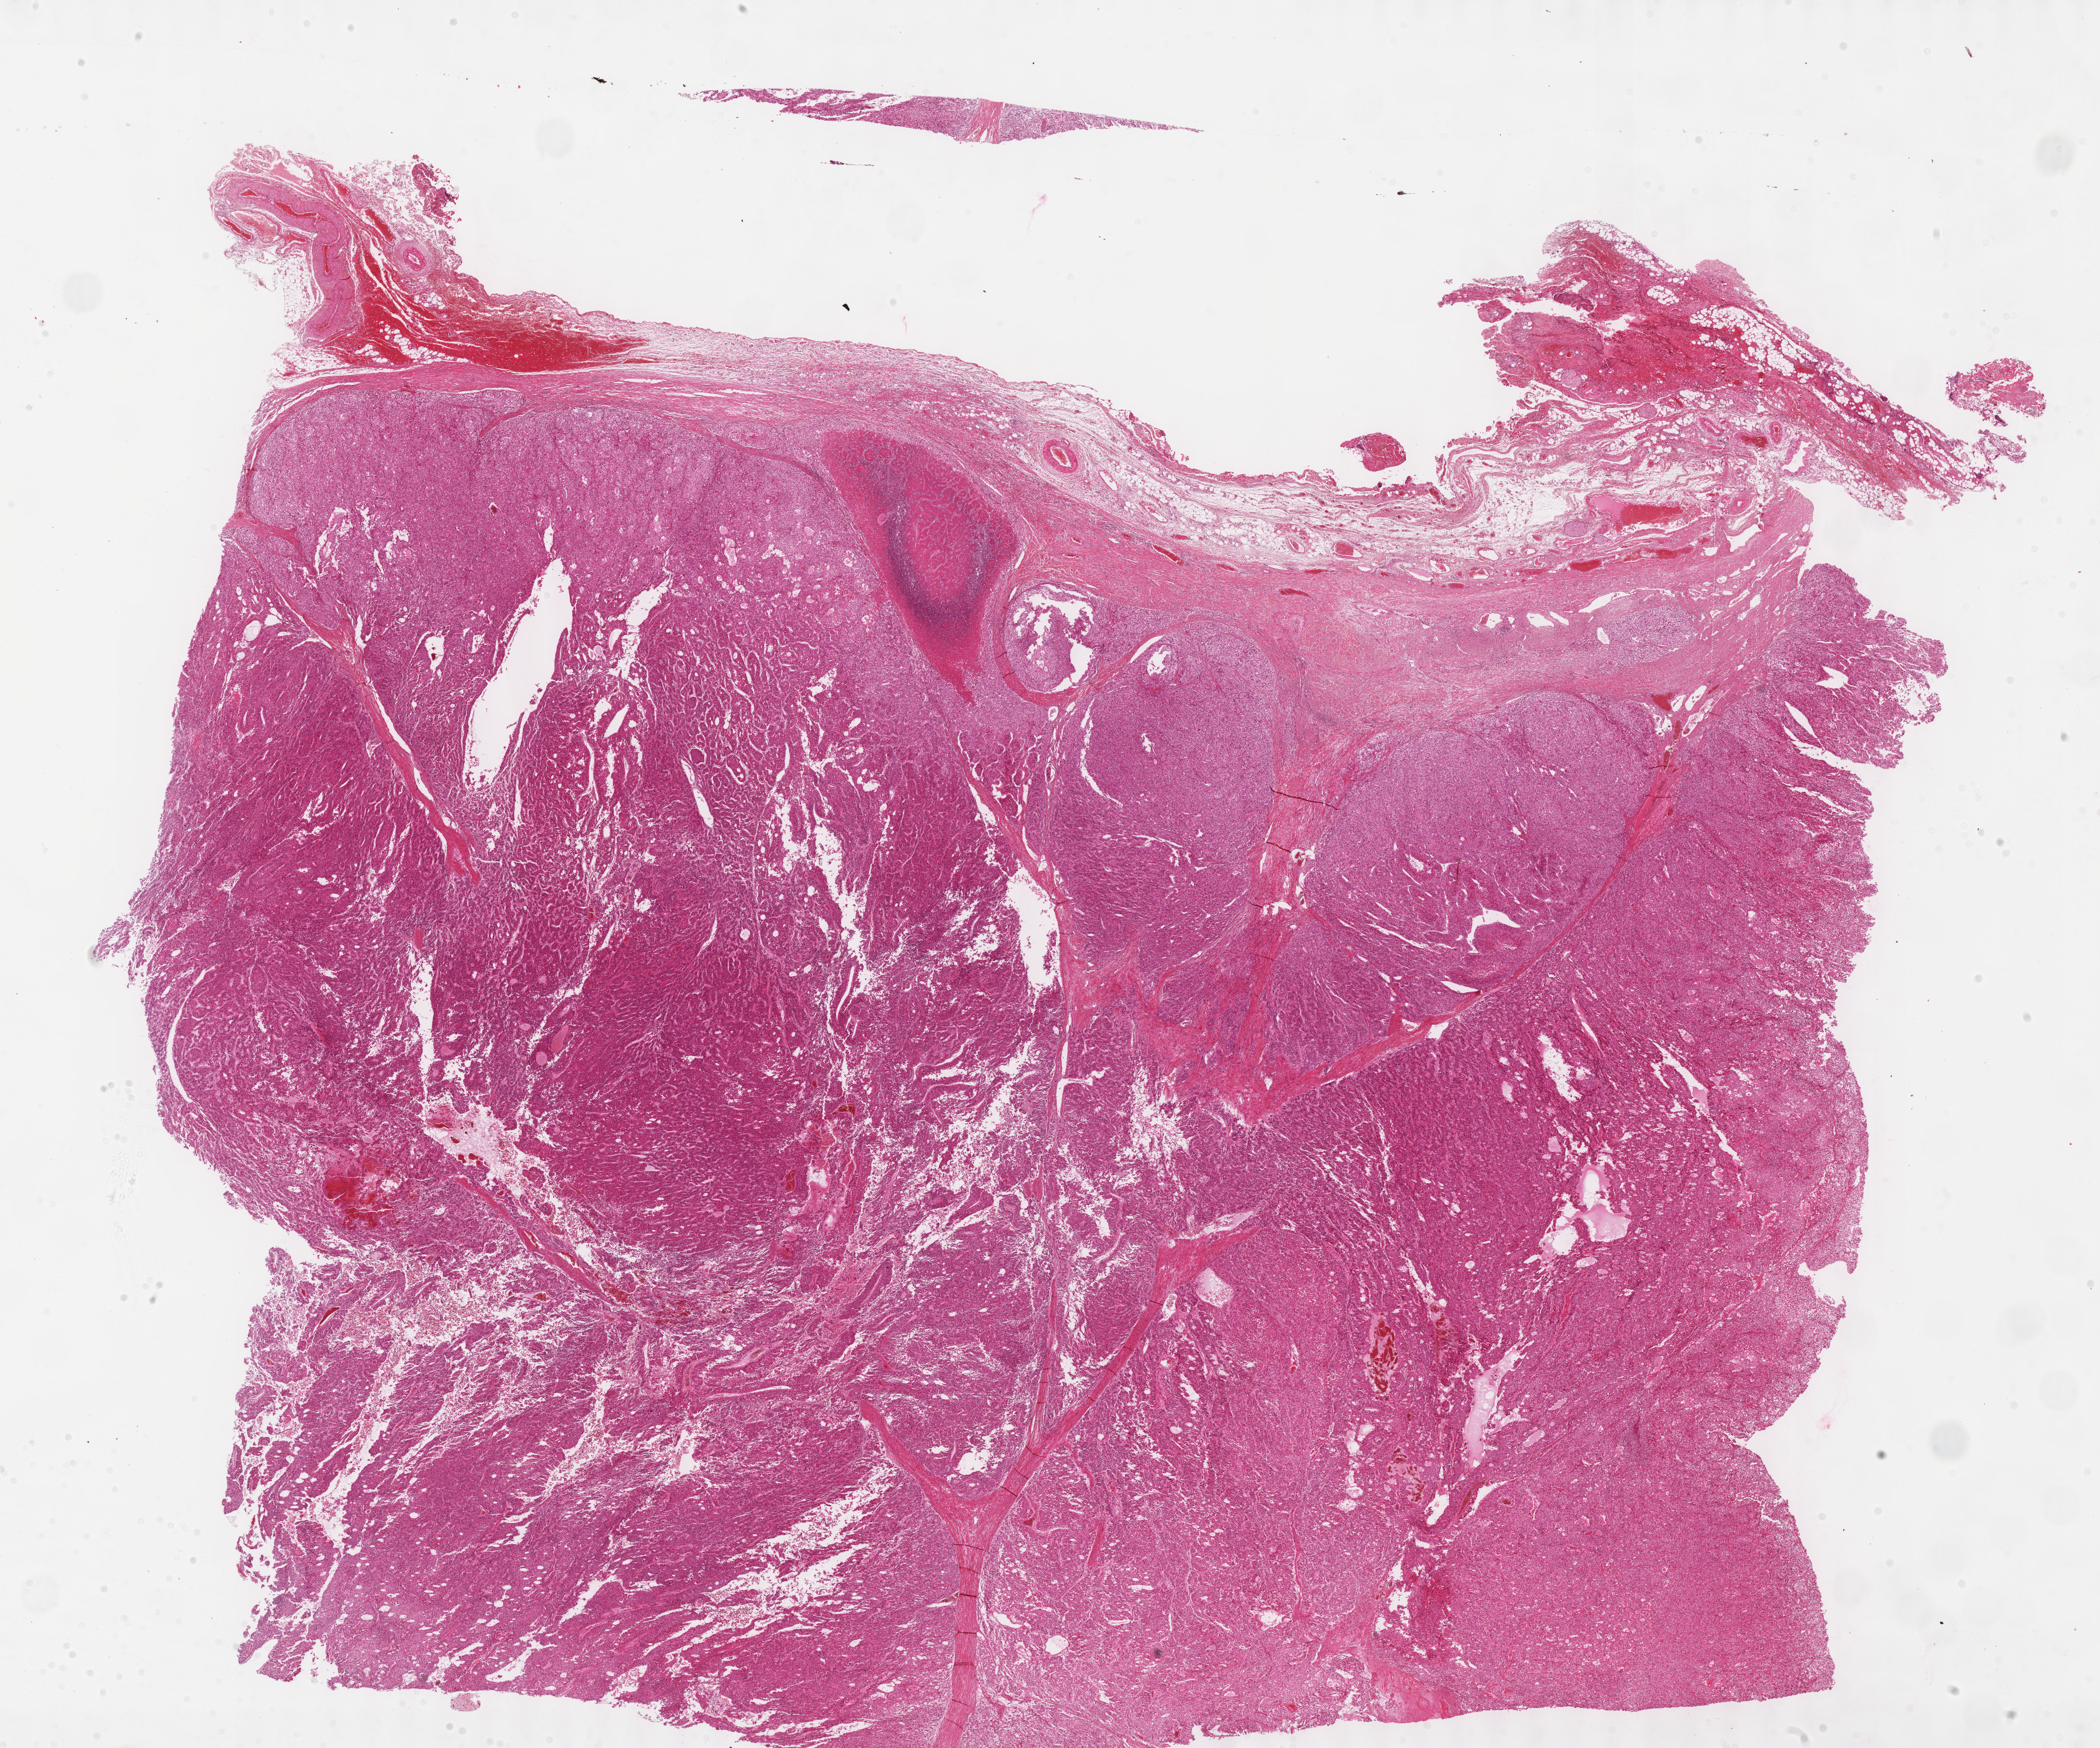
Digitized H&E-stained tissue section (whole slide), whole scanned area (about 27.2 x 22.6 mm, from a 40x scan) shown as a low-resolution overview, formalin-fixed paraffin-embedded (FFPE) diagnostic section, primary tumour sample from the adrenal cortex. Female patient; age at initial diagnosis 61 years.
- pathologic diagnosis: Adrenal cortical carcinoma (cortex of adrenal gland)